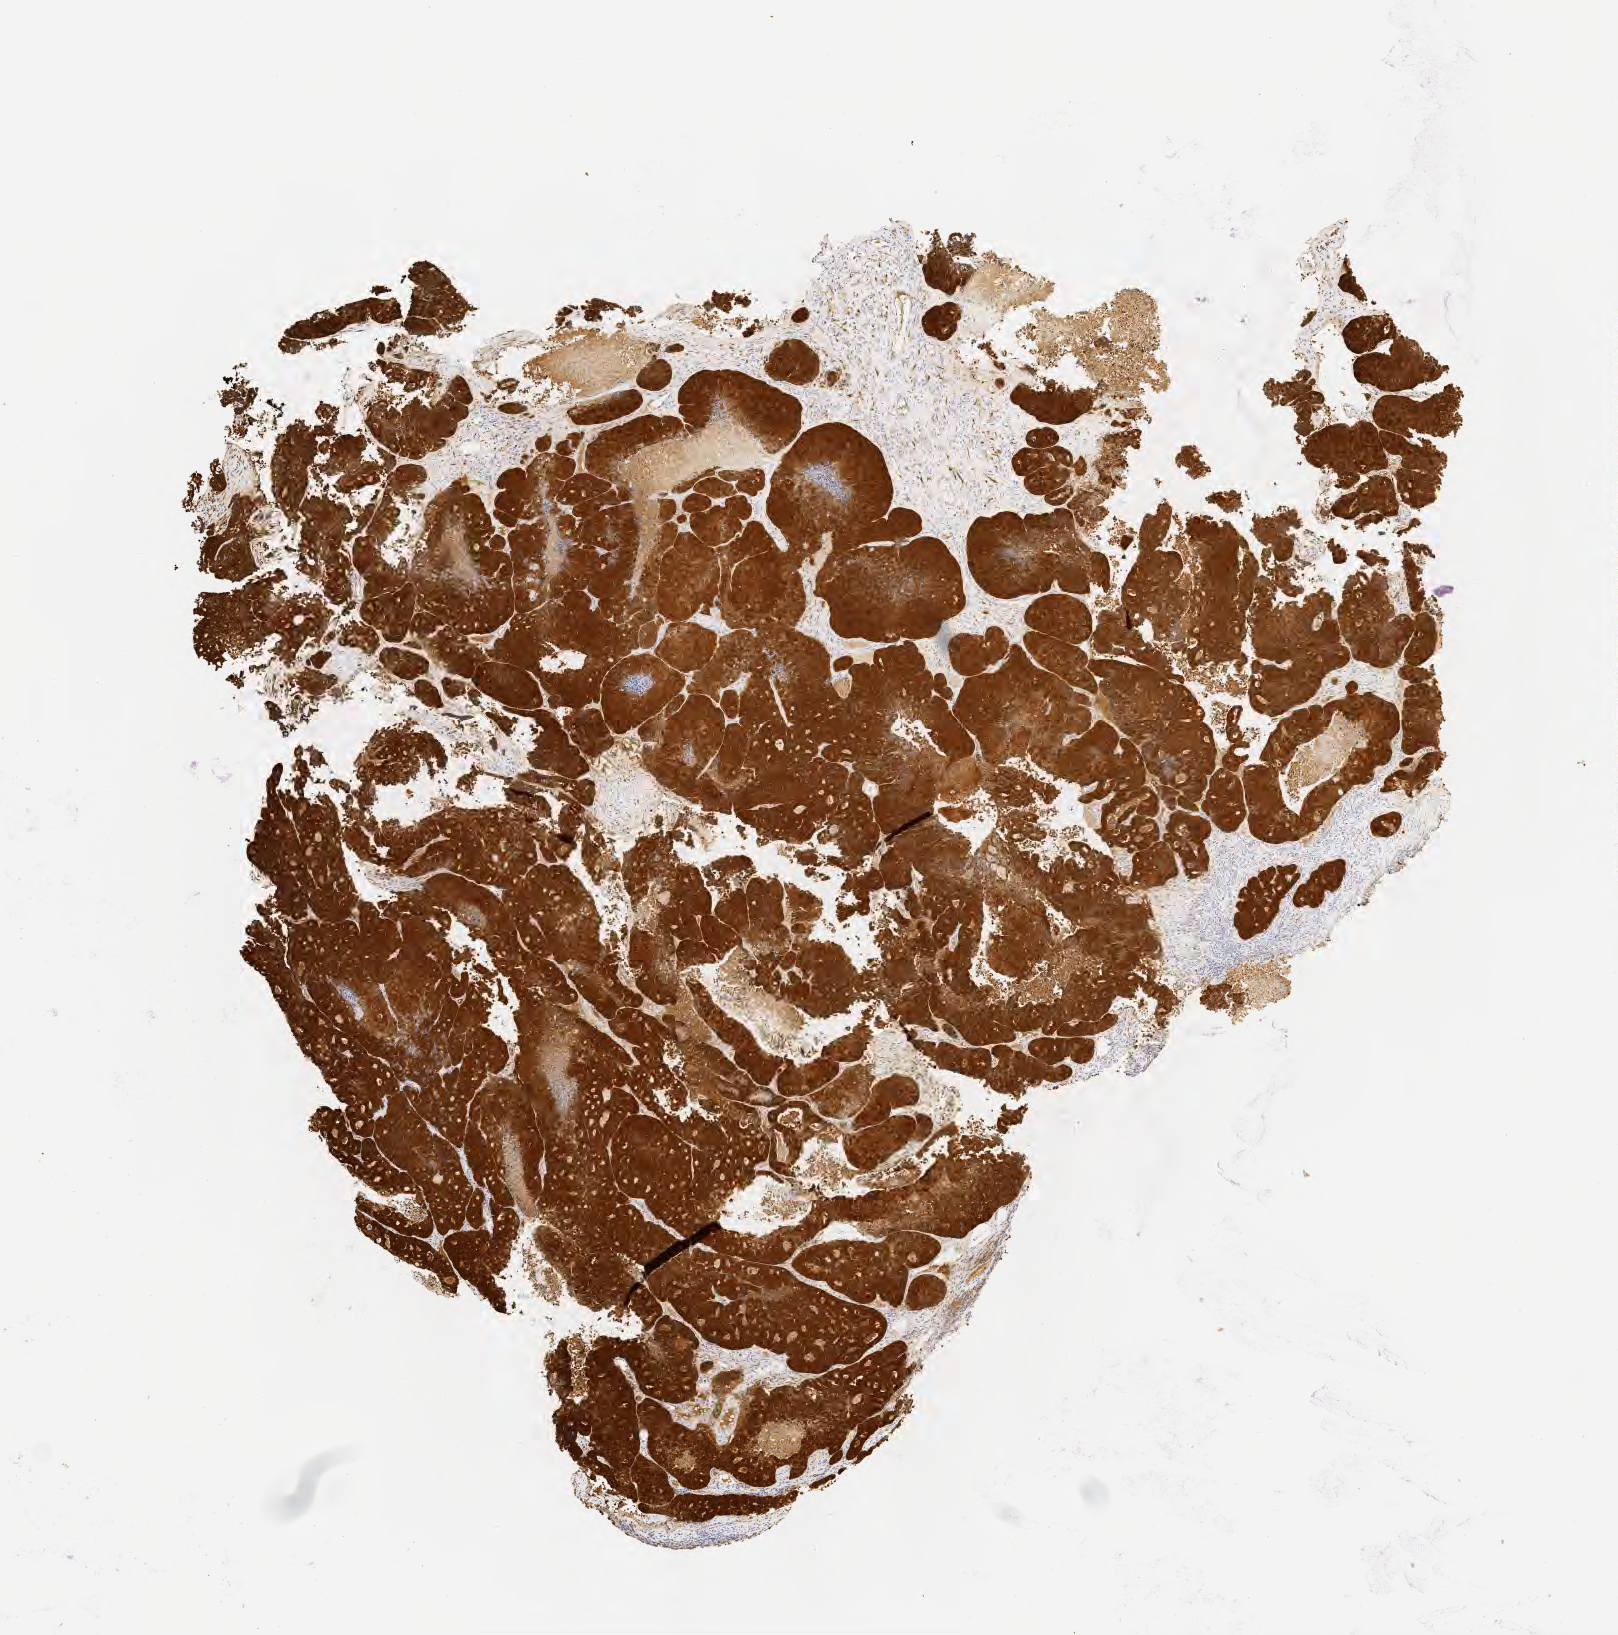
Immunohistochemistry (IHC) whole-slide image stained for p16 (p16INK4a), low-resolution overview of the scanned area, about 6.5 x 6.6 mm, specimen: tumor tissue, site: cervix. Patient female; age 48 years.
Histologic diagnosis: Adenocarcinoma, NOS.